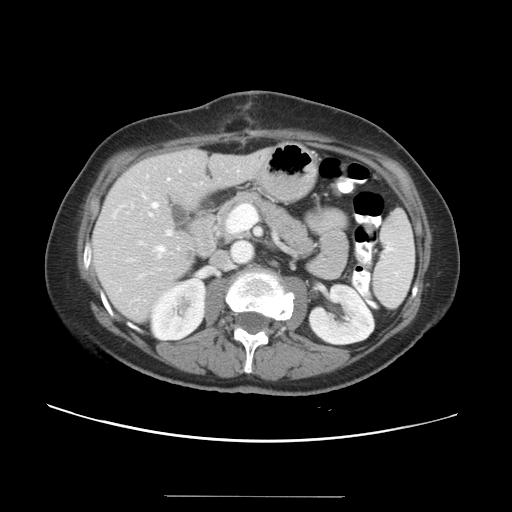
Contrast-enhanced abdominal CT, one axial slice. Reconstruction kernel STANDARD. 120 kVp. Soft-tissue window (W 400 / L 40 HU). 5 mm slice thickness. 512 × 512 image matrix, field of view 382 × 382 mm. Female patient, age 69 years. Case-level facts recorded for this patient, not image findings: diagnosis: colorectal cancer liver metastases, imaged before liver resection; multiple liver metastases: yes; largest metastasis: 1.4 cm; chemotherapy before resection: no.
Annotated regions visible in this slice (outlined manually by an expert reader):
- hepatic veins: bounding box (x1, y1, x2, y2) in pixels: (140, 179, 169, 258)
- liver: (93, 150, 270, 320)
- planned liver remnant (the part of the liver to remain after resection): (94, 150, 270, 320)
- portal vein (with intrahepatic branches): (167, 204, 258, 235)